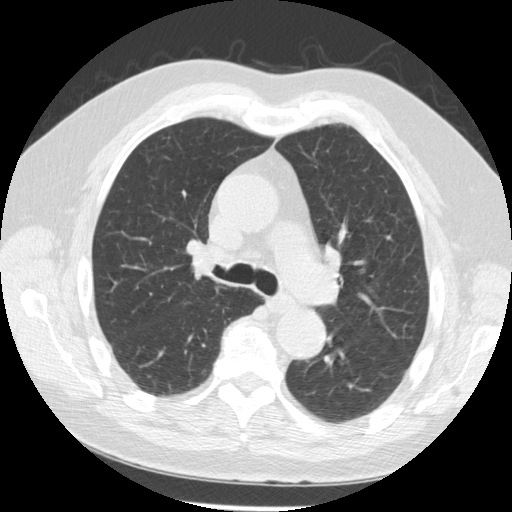
Low-dose screening chest CT, one axial slice. Reconstruction kernel STANDARD. Lung window (W 1500 / L -600 HU). 2.5 mm slice thickness. 512 × 512 image matrix.
Annotated regions visible in this slice (outlined manually by an expert reader):
- lesion 2 (tumor, hilum of right lung): bounding box [x1, y1, x2, y2] px = [193, 242, 216, 273]